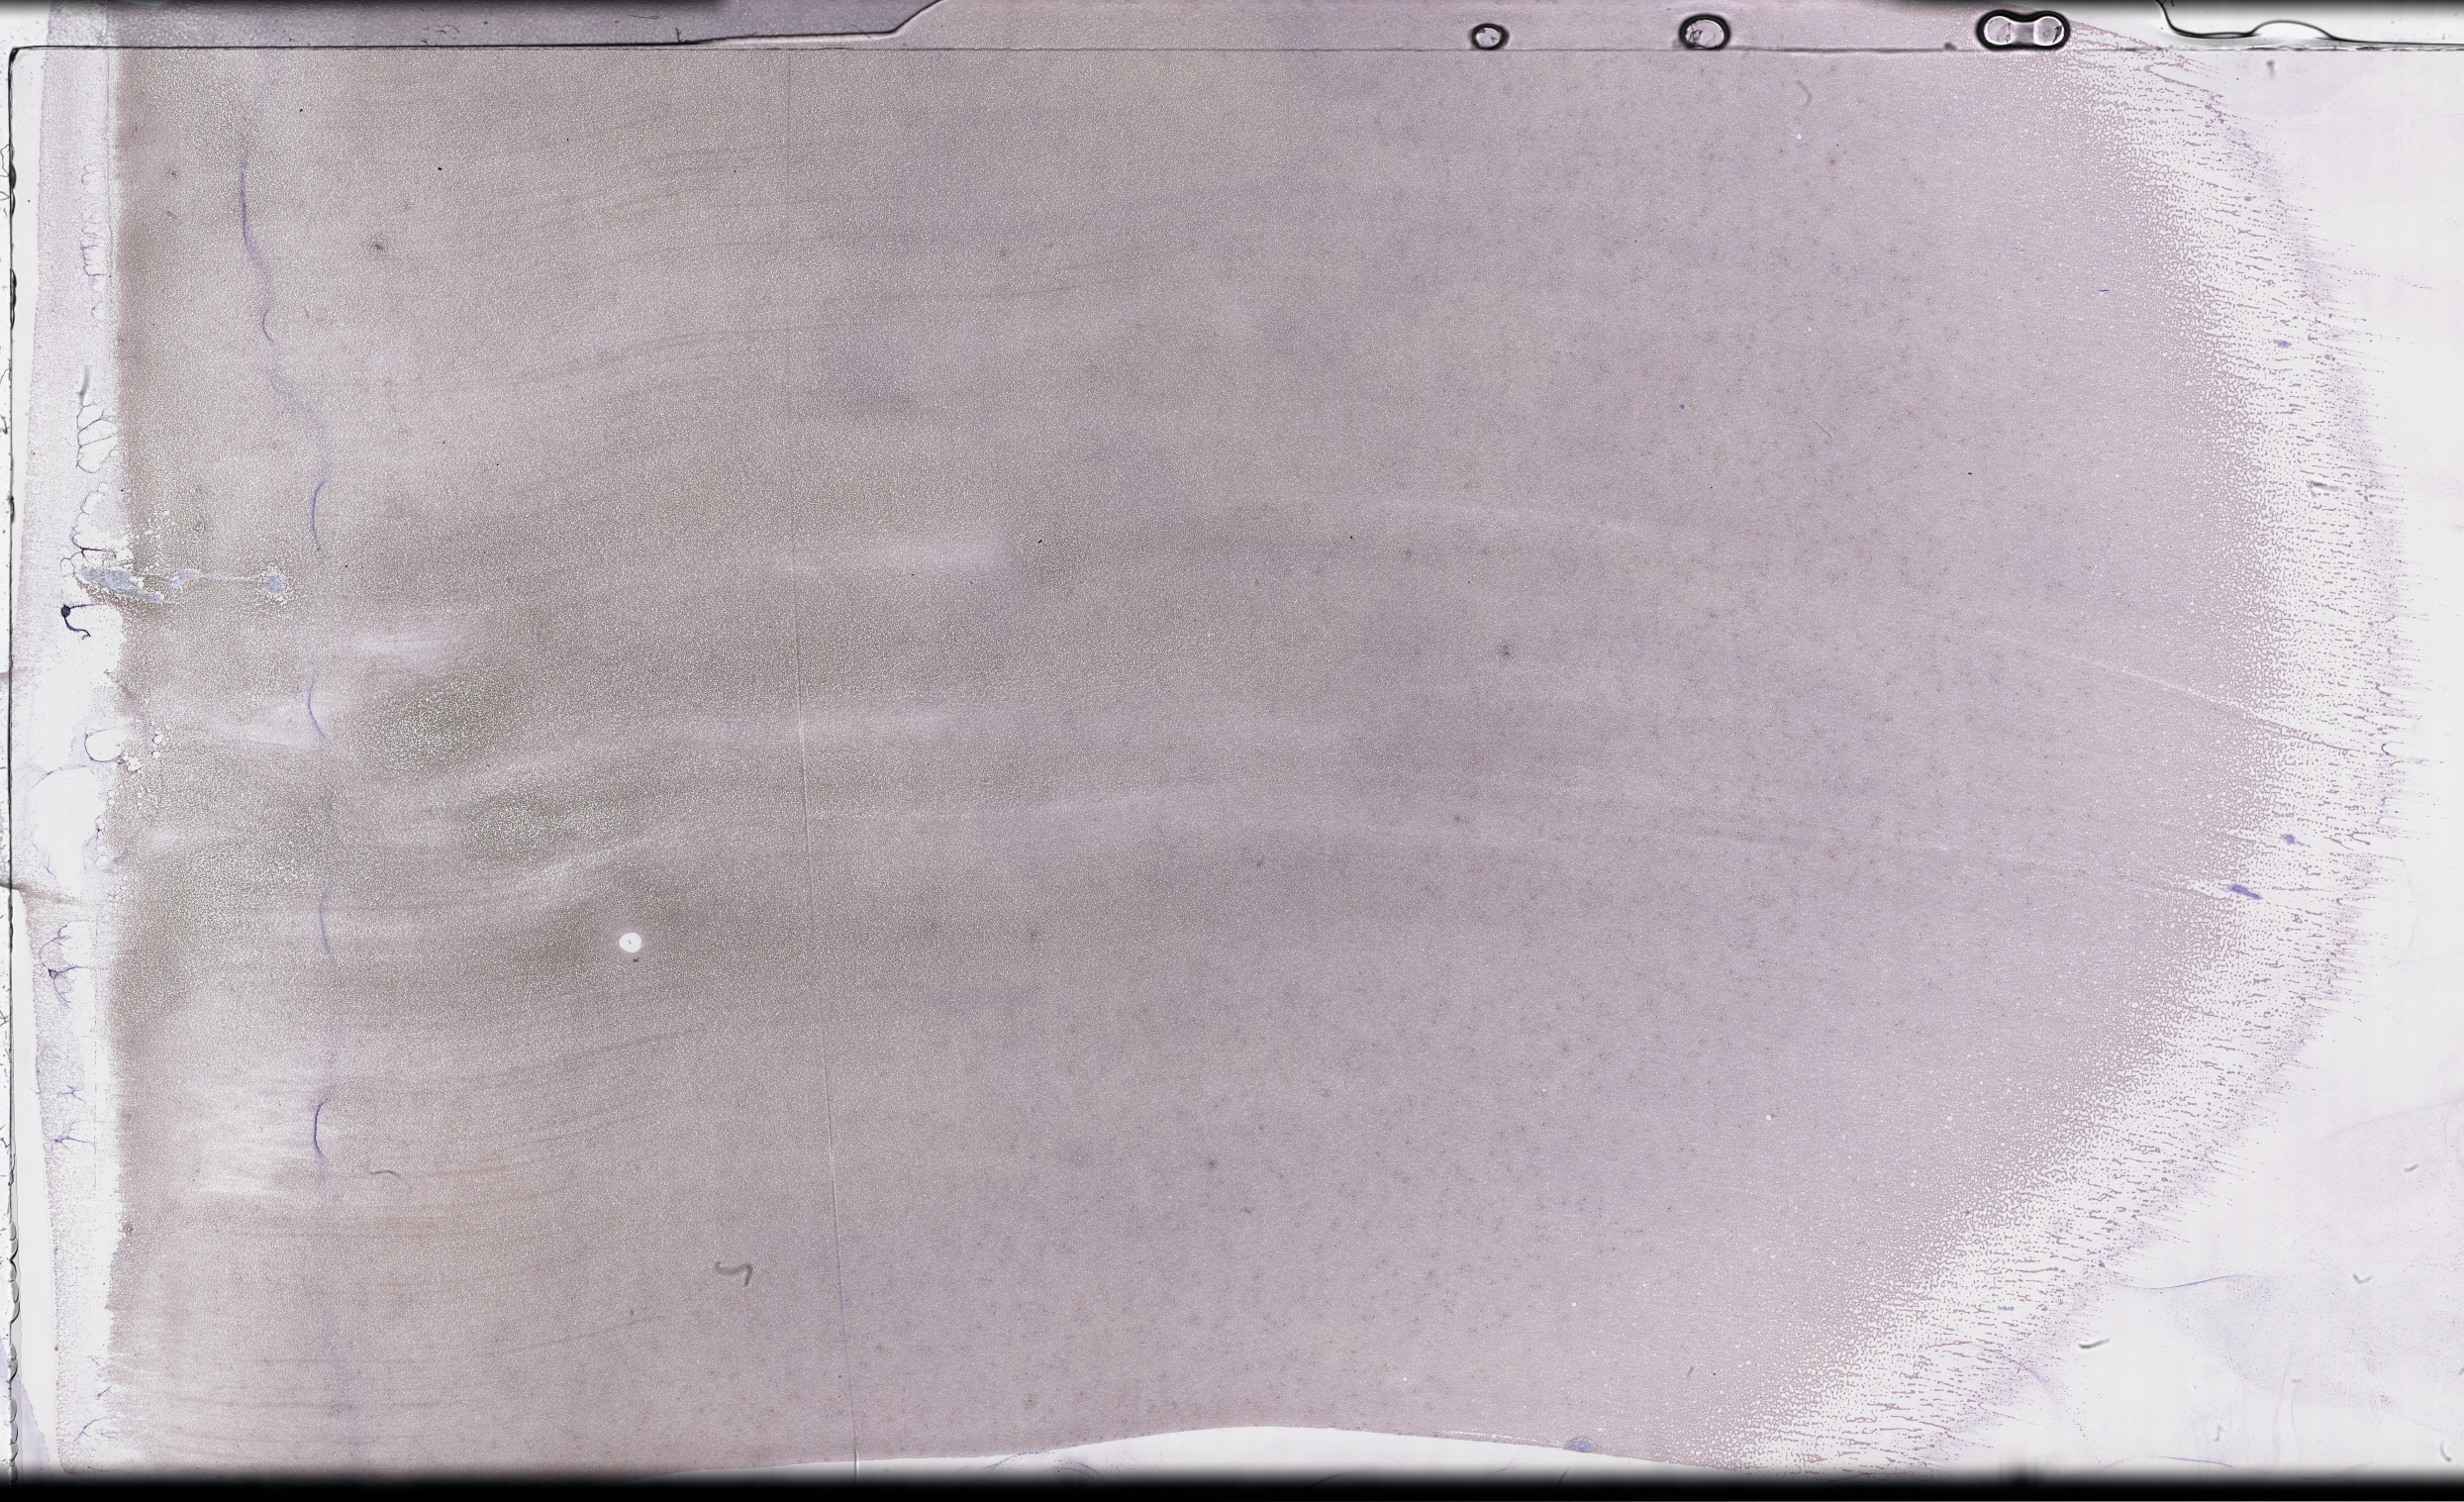
Whole-slide image of a whole blood smear, Wright-Giemsa stain — low-resolution overview of the scanned area, about 40.2 x 24.5 mm, specimen time point: collected on treatment. Patient sex: male.
From a patient with: Plasma Cell Myeloma.